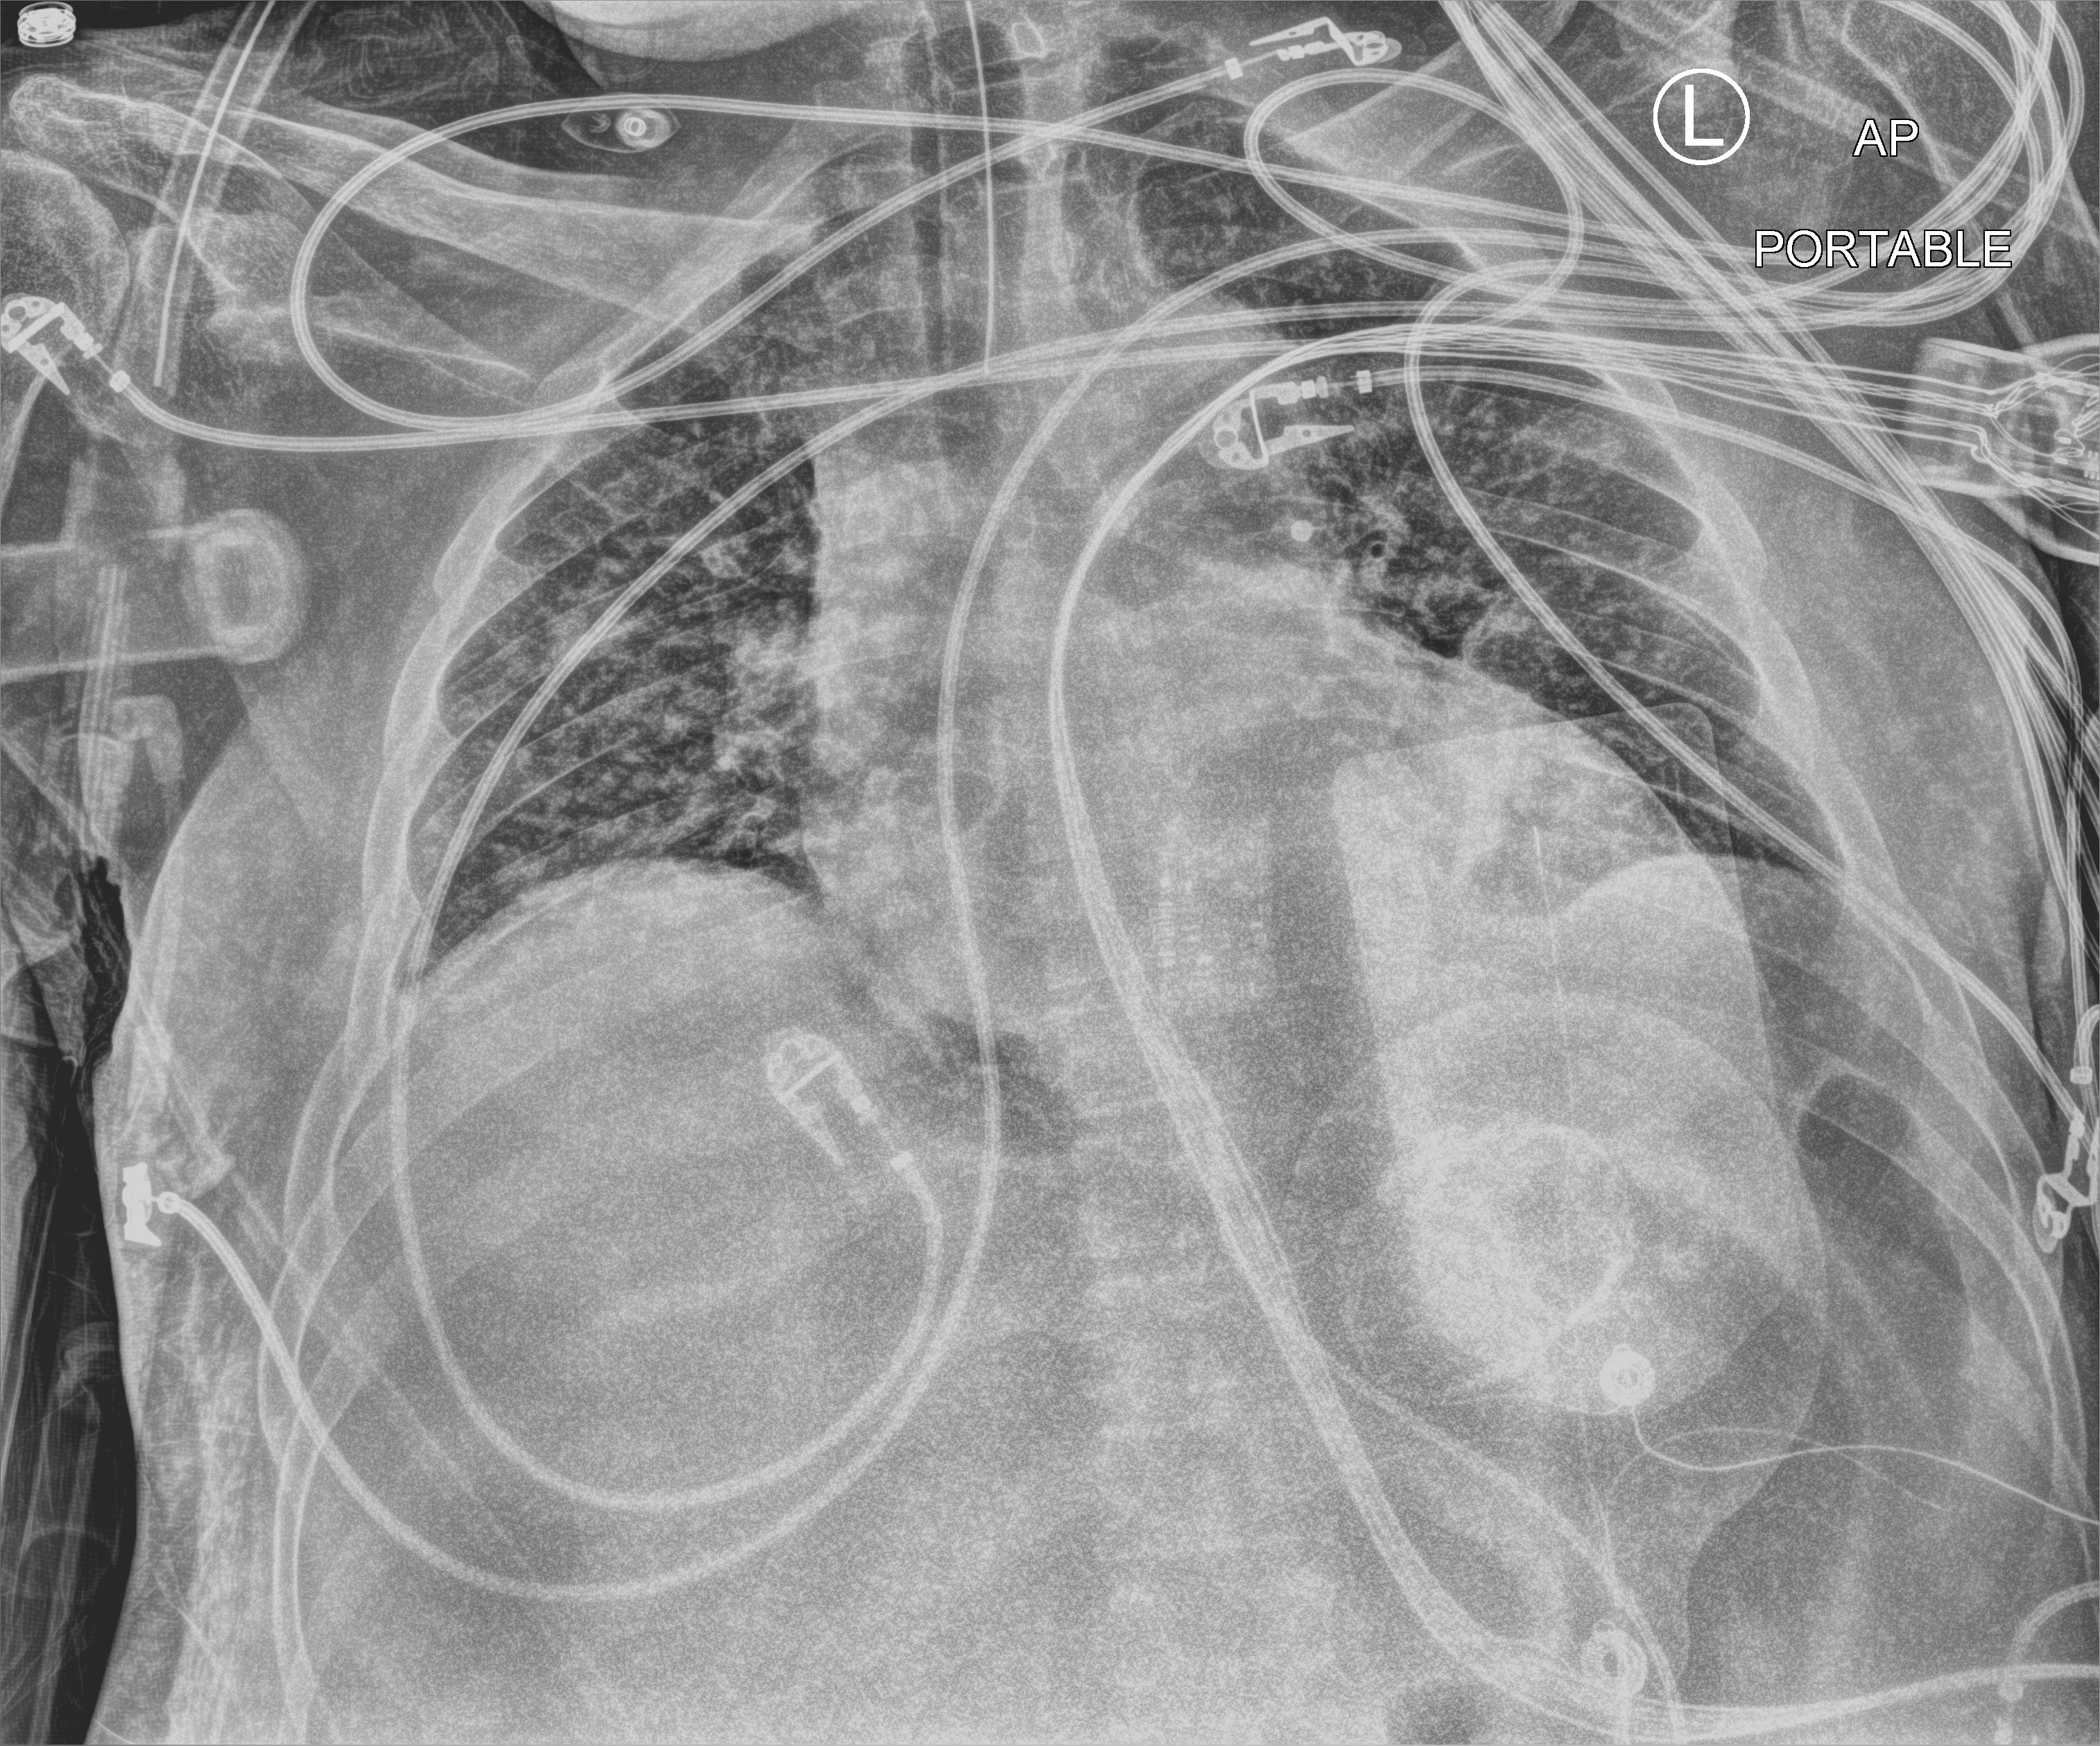
Chest X-ray (portable); anteroposterior (AP) projection. Male patient hospitalised with COVID-19, age 60–74 years.
Hospital-stay facts (about this admission, not read from this image; timing relative to this image not recorded):
- admitted to intensive care during this hospital stay: yes
- mechanically ventilated during this hospital stay: yes